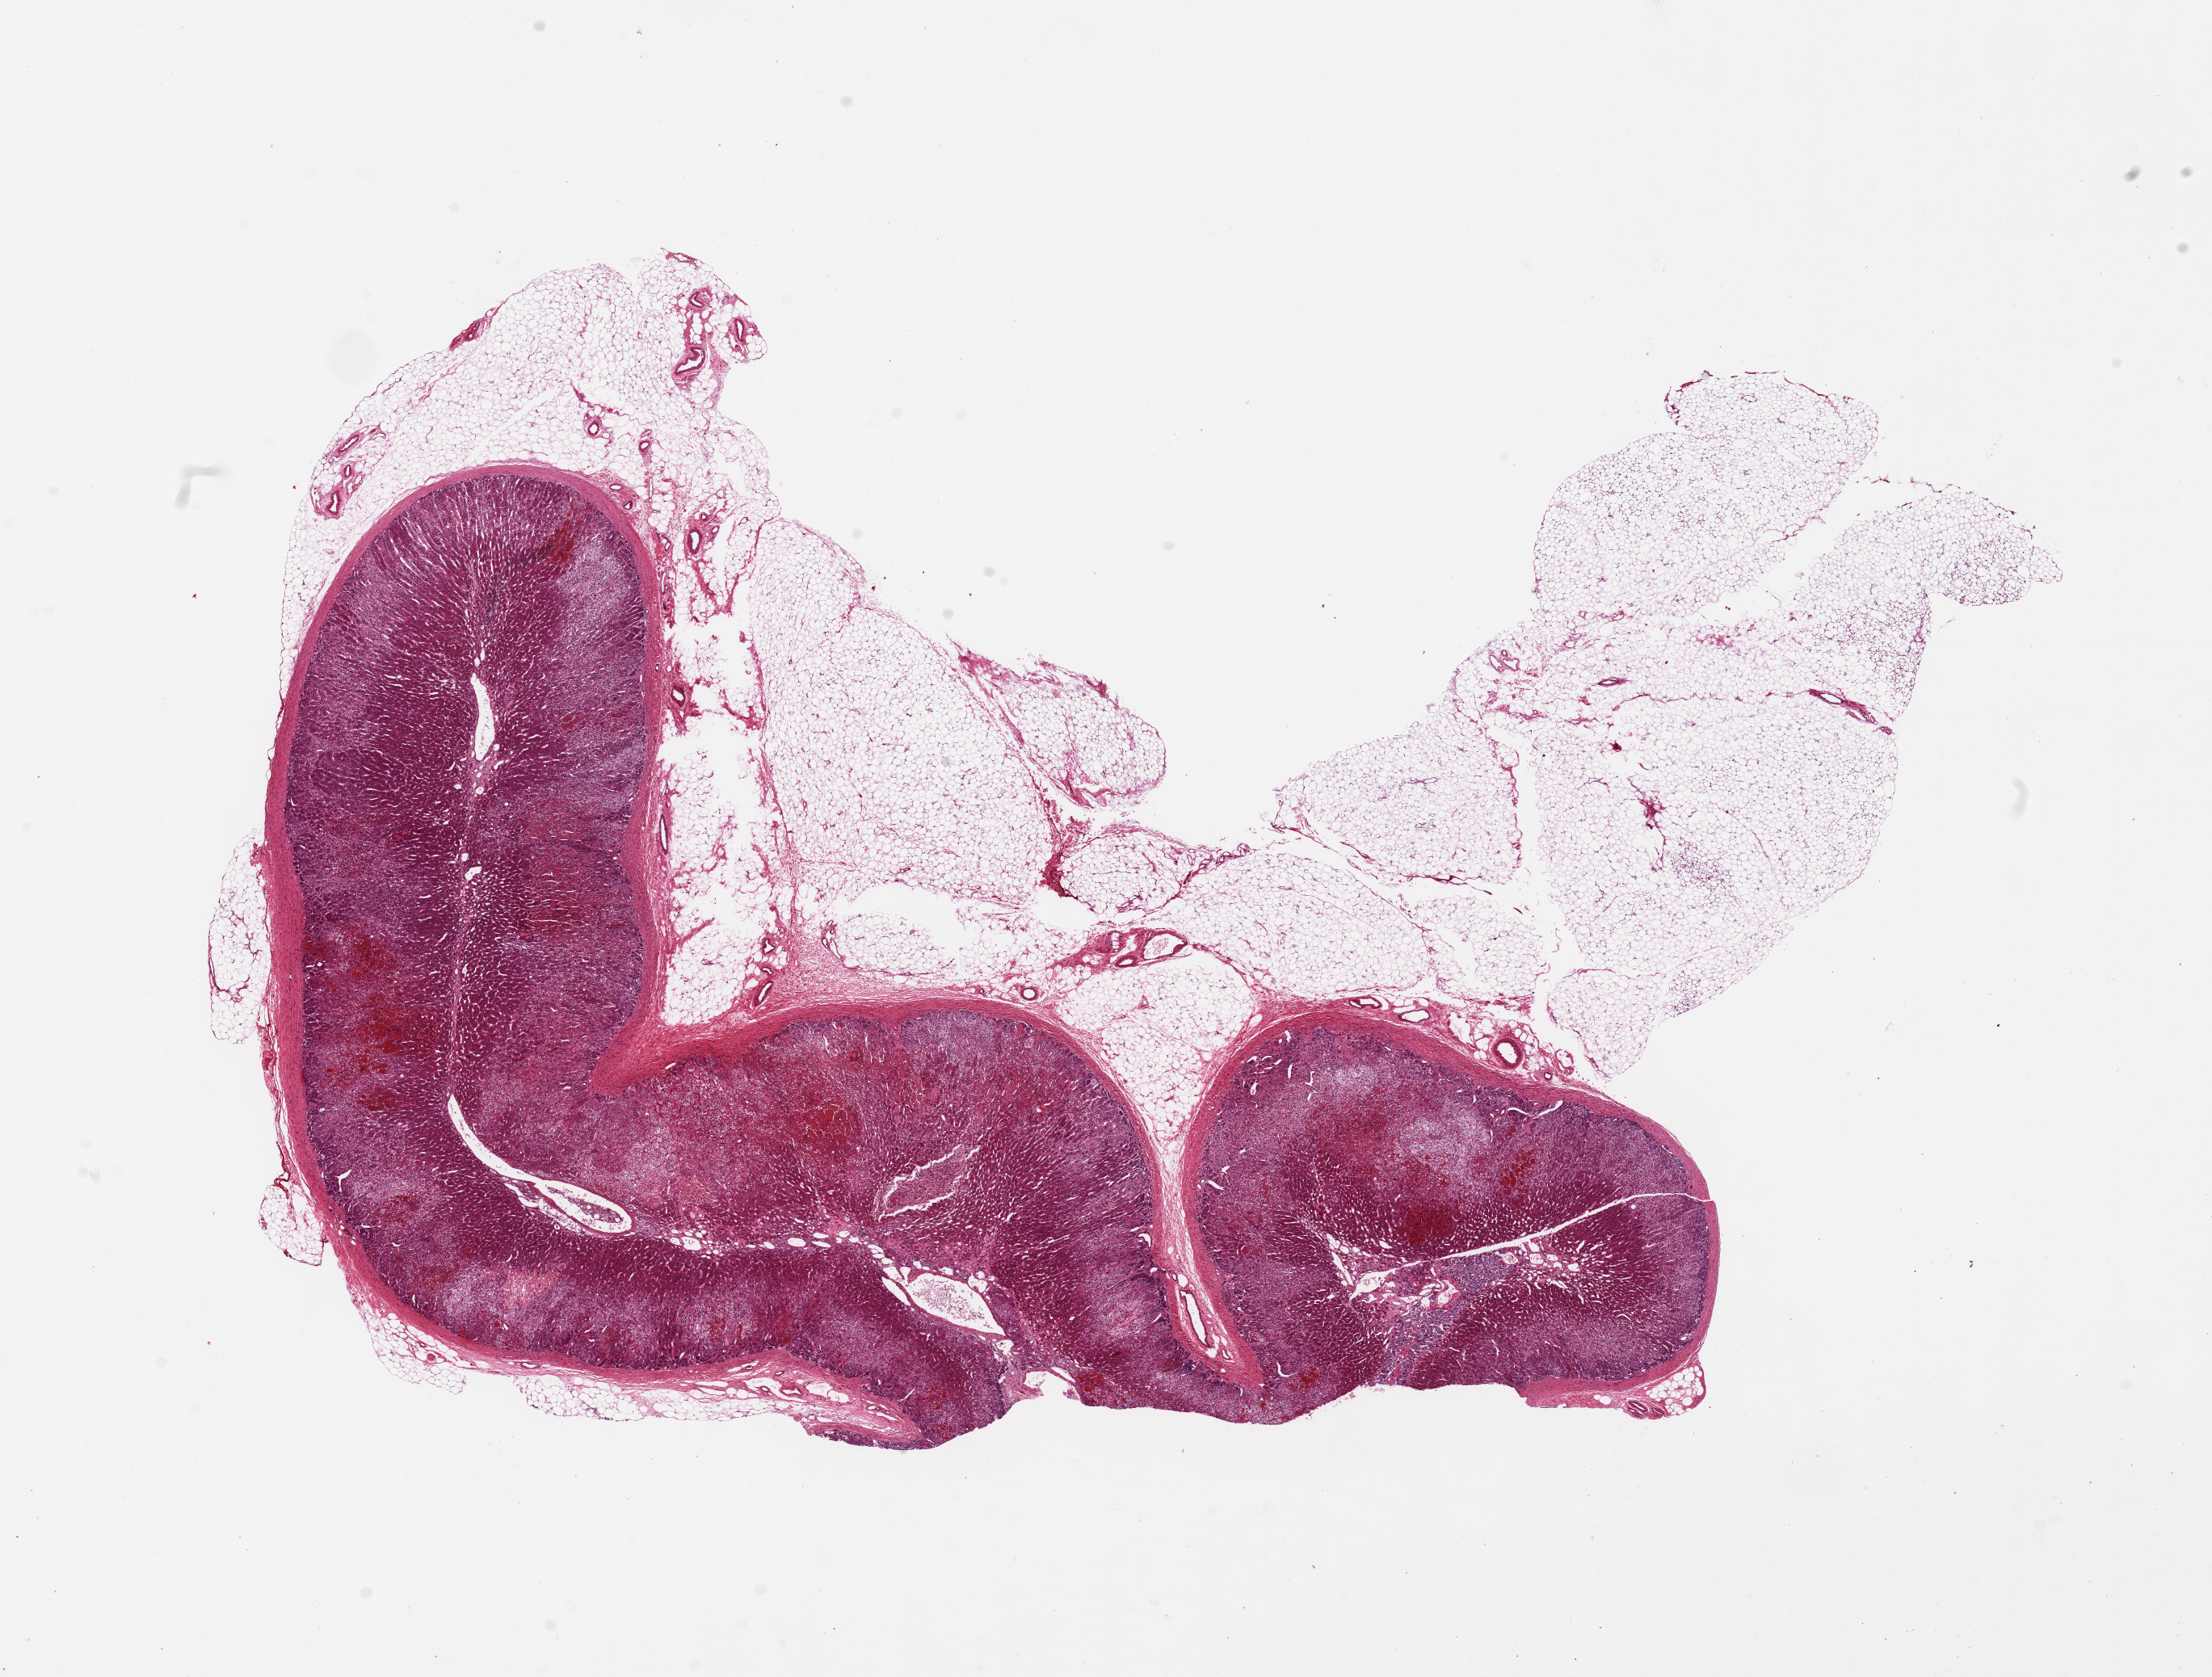
Whole-slide image, haematoxylin and eosin stain — a low-resolution overview of the entire scanned area, about 21.7 x 16.4 mm. PAXgene-fixed, paraffin-embedded tissue. Target tissue: adrenal gland. Tissue donor sample. Donor: male.
Review note (as recorded): 1-2. 15.2 x 15.7 mm. Focal area centrally with poor fixation.